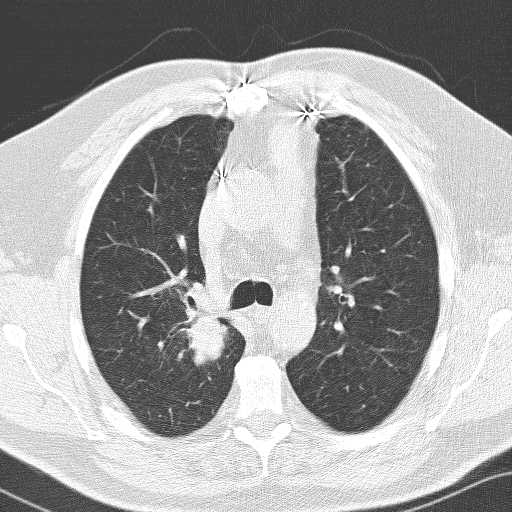
Axial slice from a low-dose chest CT screening exam, first (baseline) screen, lung window (W 1500 / L -600 HU), 3.2 mm slice thickness, lung (sharp) reconstruction kernel (D), 120 kVp, slice 40 of 141 in the series, 512 × 512 image matrix. Male participant, aged 66 years at enrolment. Former smoker at enrolment.
Lesion marked by an expert reader, bounding box (x1, y1, x2, y2) in pixels: (146, 295, 232, 390). Reader record for this screening exam (exam-level; its link to the box is not recorded): non-calcified nodule or mass ≥4 mm, right upper lobe, 36 × 30 mm, spiculated (stellate) margins, soft tissue attenuation. Later outcome: lung cancer diagnosed 103 days after this screen — adenocarcinoma, NOS, right upper lobe, poorly differentiated (G3), stage IIB (AJCC 6th edition), 33 mm at pathology.